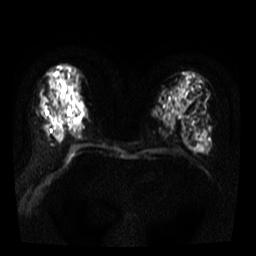
Breast MRI, one axial slice; slice 18 of 38 in the series (ordered by position); diffusion-weighted series; image 2 of 4 stored at this slice position (different b-values; order by instance number); 3 T; 5 mm slice thickness; 256 × 256 image matrix. Female patient.
Structures marked on this image (expert manual segmentation):
- tumour on diffusion-weighted imaging: bounding box (x1, y1, x2, y2) in pixels: (205, 142, 207, 146)